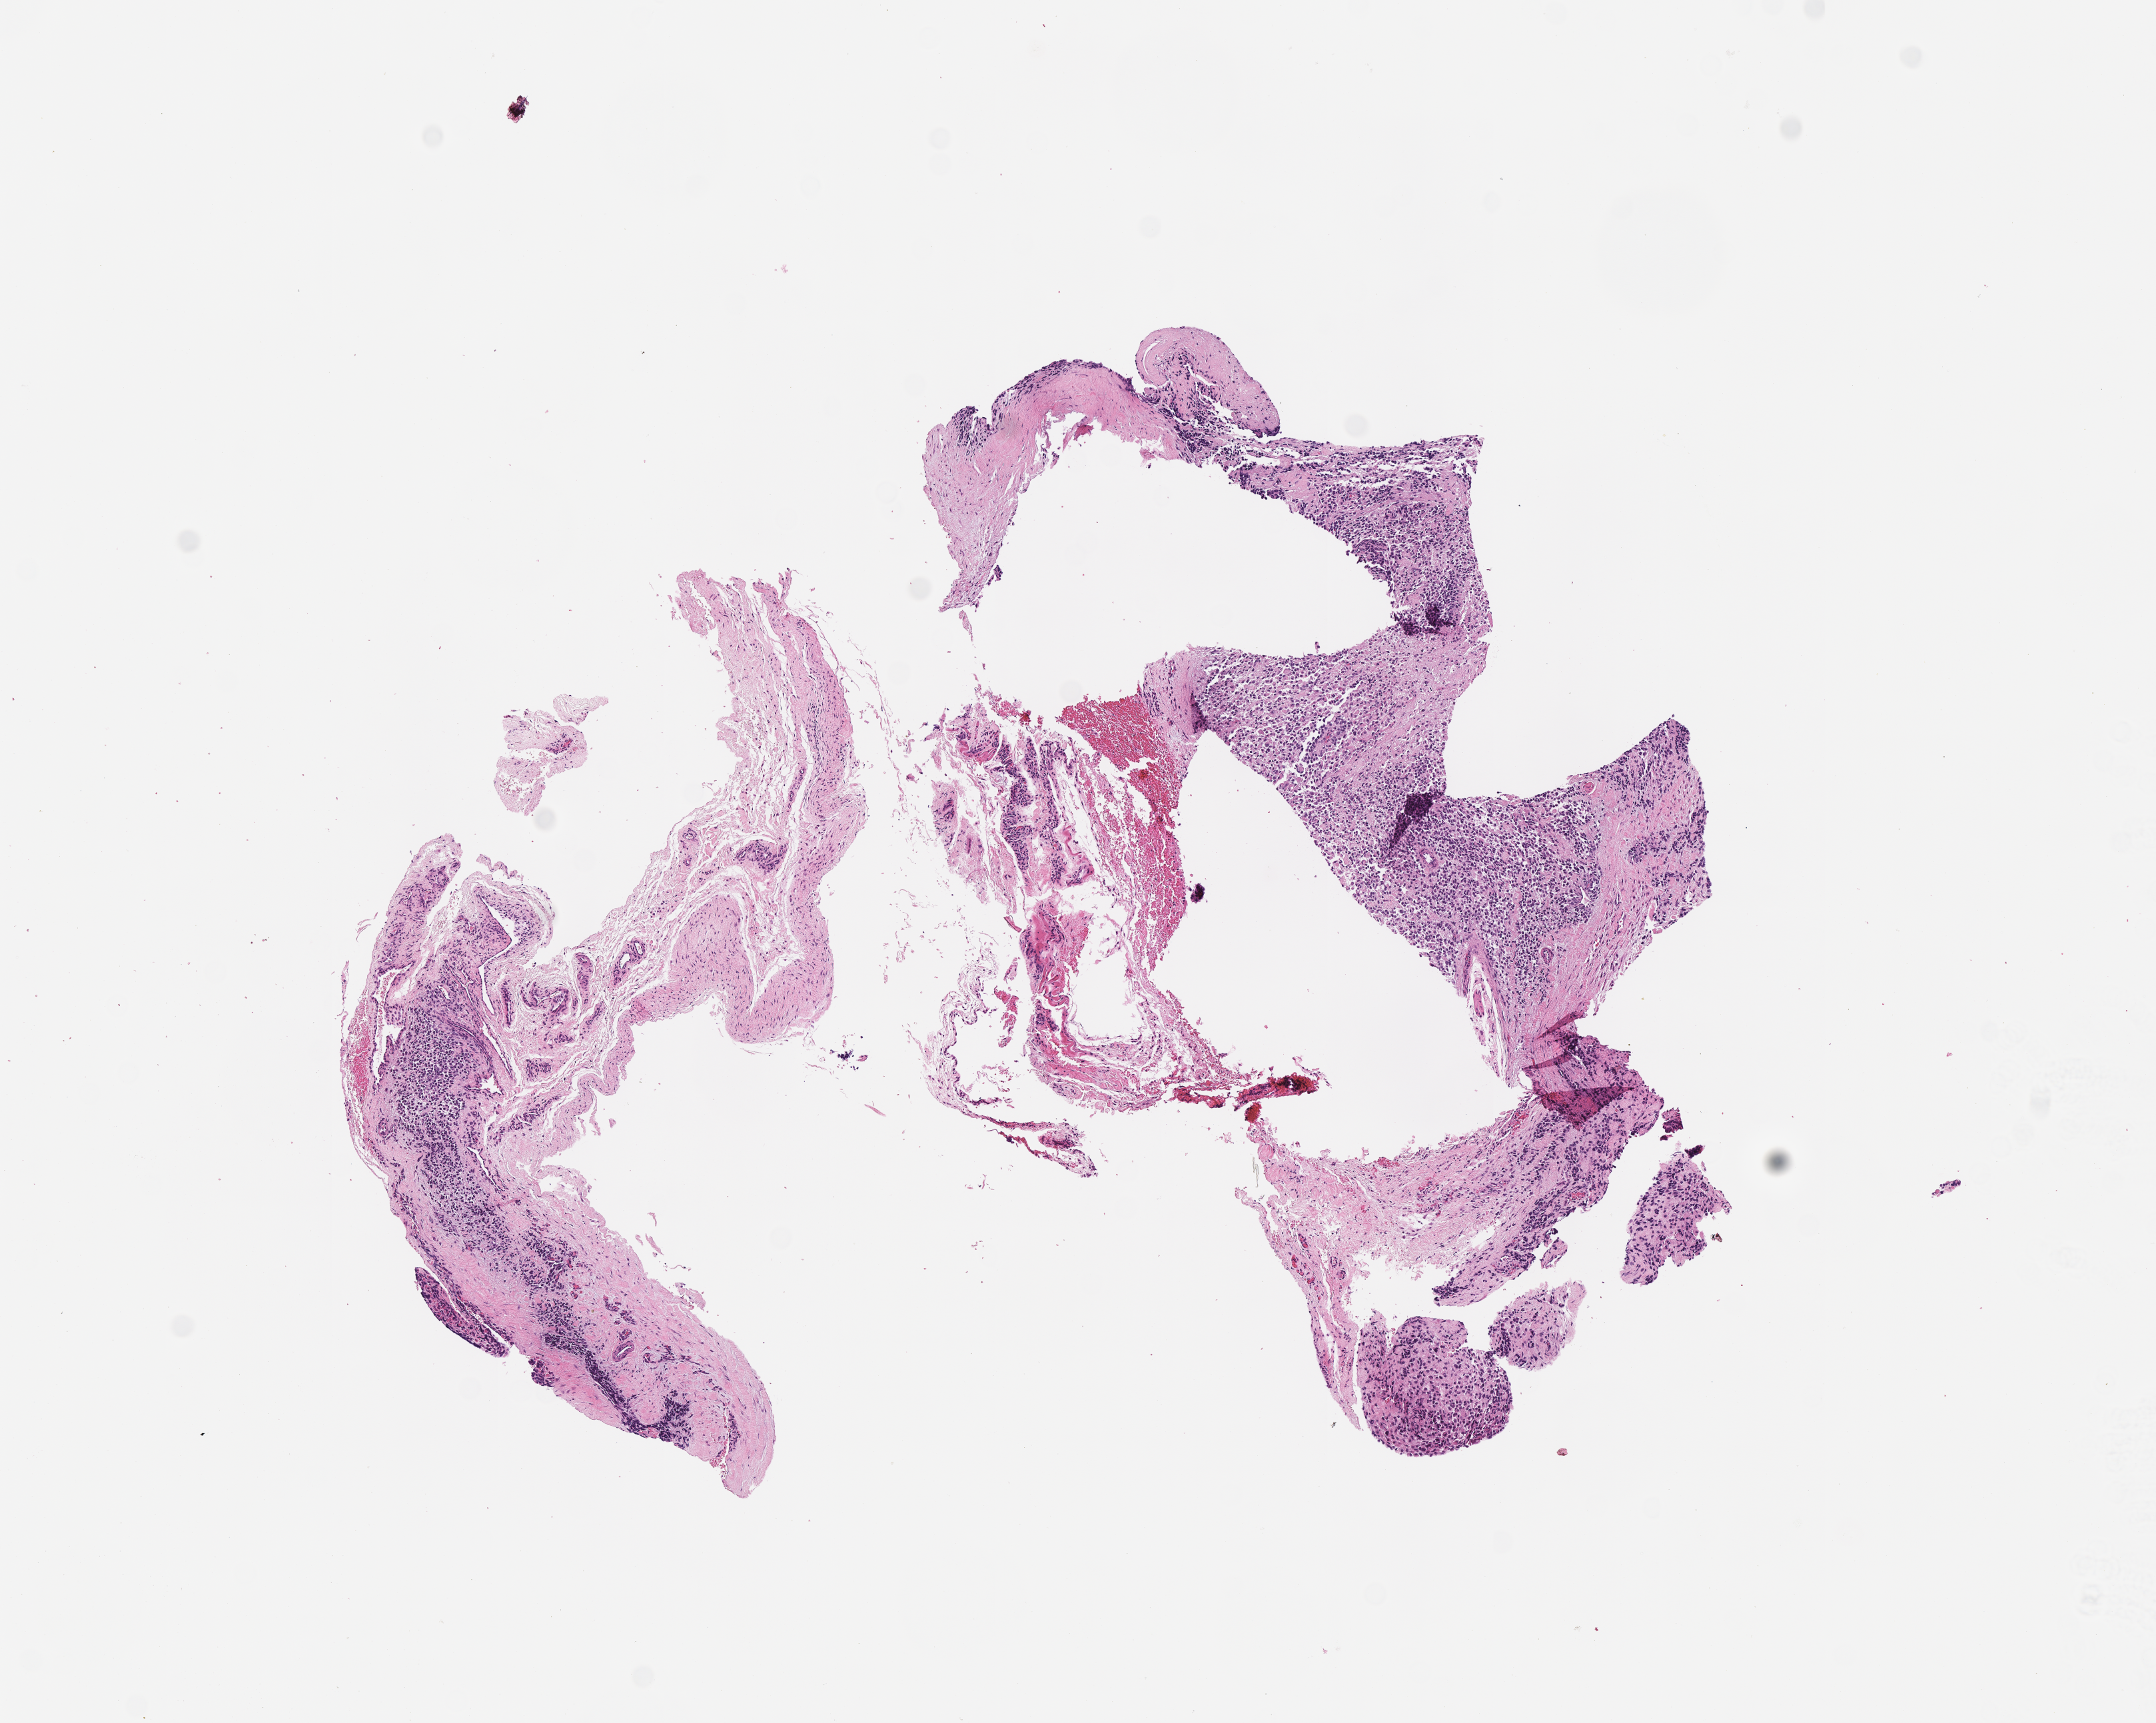
Haematoxylin and eosin whole-slide image of tumor tissue, shown as a low-resolution overview of the whole scanned area (about 6.5 x 5.2 mm). FFPE section. Sample anatomic site: soft tissue, foot-right. Male patient, age at diagnosis 17.2 years.
Metastatic status at presentation (as recorded): metastatic (confirmed). Stage (as recorded): 4. Diagnosis: rhabdomyosarcoma; histological classification: alveolar rhabdomyosarcoma.